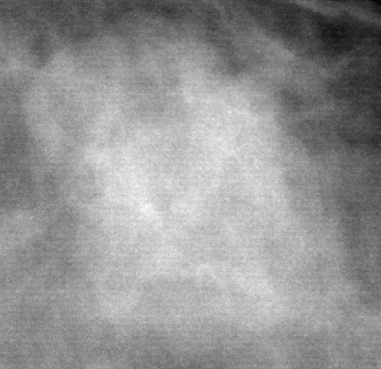
Crop from a digitized film mammogram around one marked abnormality; left breast; CC view; BI-RADS breast density category 1 (scale 1–4).
Marked abnormality: mass, shape lobulated, margins obscured; BI-RADS assessment category 3; subtlety rating 5 on a 1 (subtle) to 5 (obvious) scale; pathology (as recorded): benign.